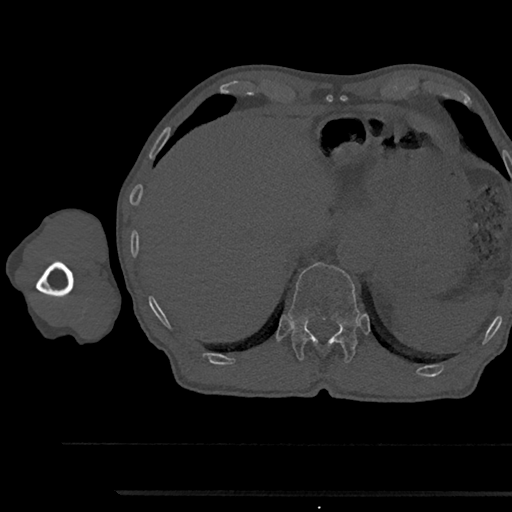
CT including the spine, one axial slice; slice 732 of 797 in the series (ordered by position); 120 kVp; bone window (W 1800 / L 400 HU); 0.5 mm slice thickness; 512 × 512 image matrix. Patient: male, 79 years. From the clinical record (not read from this slice): primary cancer: prostate.
Outlined on this slice (semi-automatically segmented with operator editing):
- T12 vertebra: bounding box (x1, y1, x2, y2) in pixels: (288, 262, 359, 363)